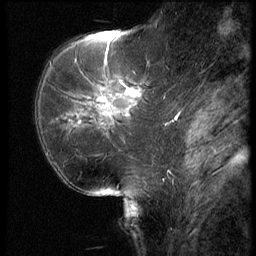
Breast MRI (dynamic contrast-enhanced), one sagittal slice. Position 22 of 62 along the scan axis. 3 images stored at this slice position (order not interpretable as contrast timing). 1.5 T. TE 4.2 ms, TR 9 ms. 2.5 mm slice thickness. 256 × 256 image matrix, field of view 180 × 180 mm. Female patient, age 62 years. From the clinical record (not read from this slice): setting: breast cancer imaged before/during neoadjuvant chemotherapy; receptor status: HR-positive, HER2-negative.
Annotated regions visible in this slice (semi-automatically segmented with operator editing):
- analysis volume of interest (the breast-tissue region the enhancement analysis was run in; not a lesion): box from (x=56, y=62) to (x=154, y=155) px
- tumour enhancement mask (voxels above the 140 % enhancement threshold inside the analysis volume of interest): (x=65, y=89)–(x=135, y=119)